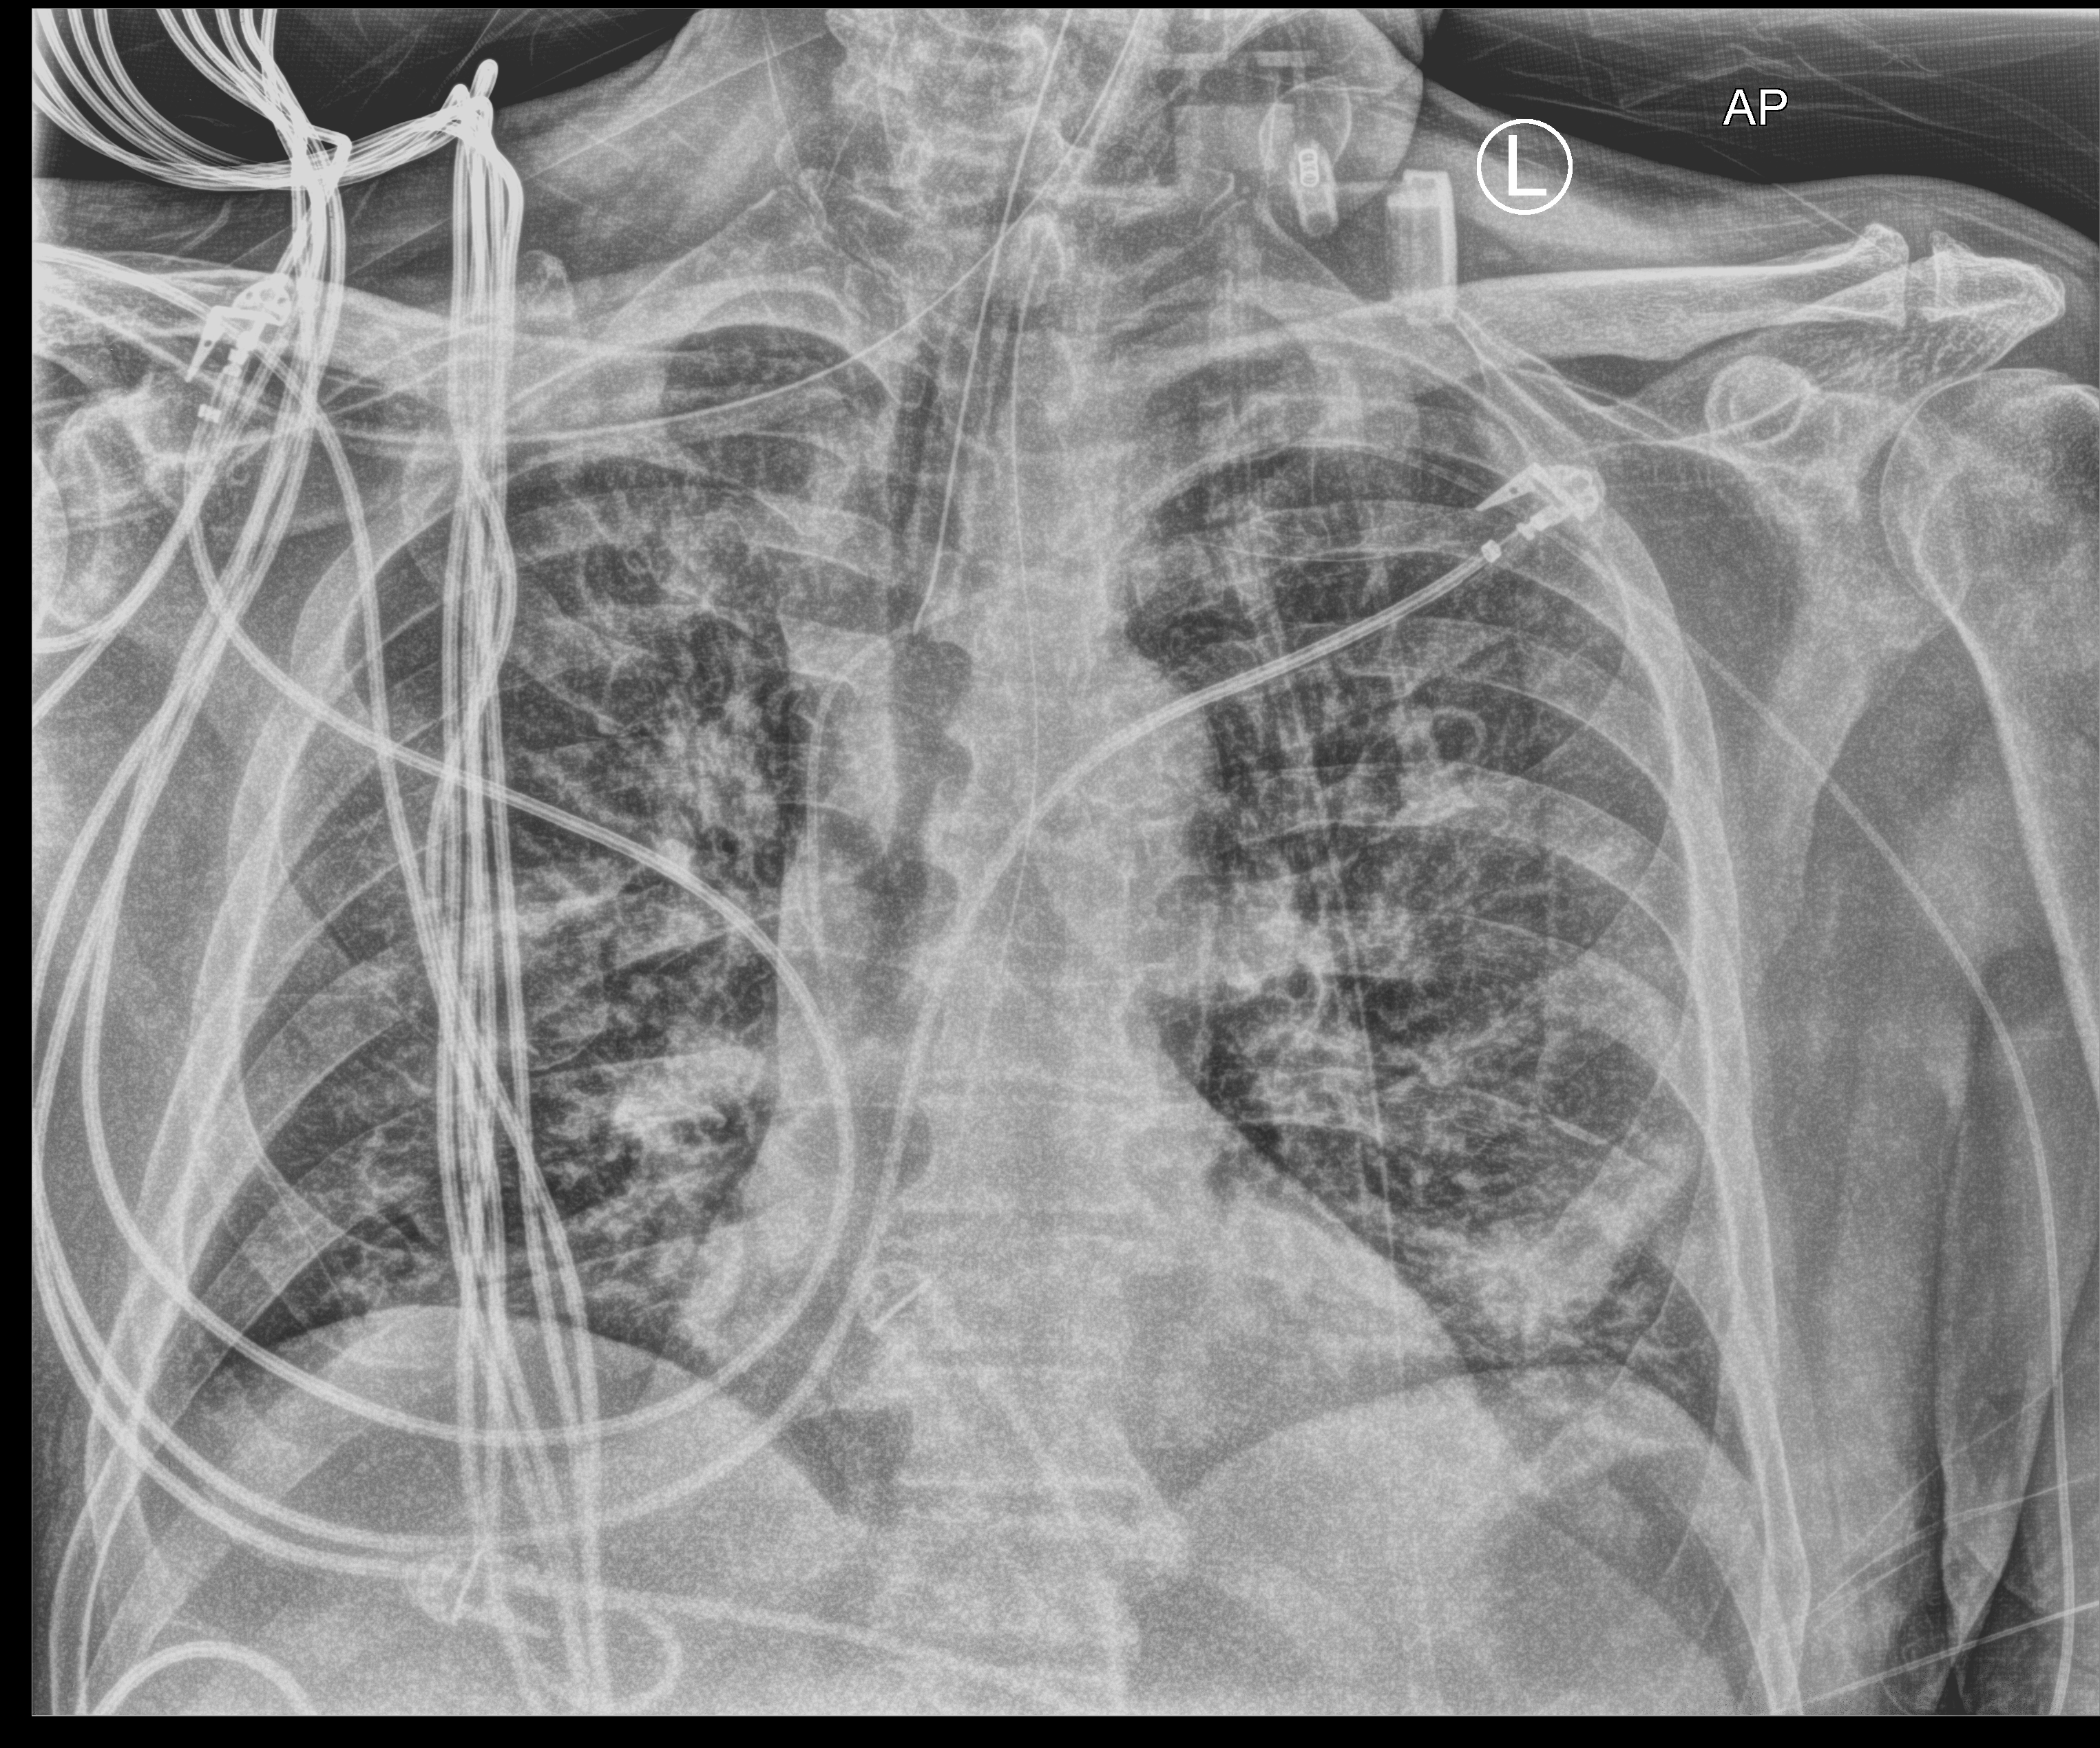
Chest X-ray (portable); anteroposterior (AP) projection. Male patient hospitalised with COVID-19, age 60–74 years.
Hospital-stay facts (about this admission, not read from this image; timing relative to this image not recorded): hypertension (admission record): yes.